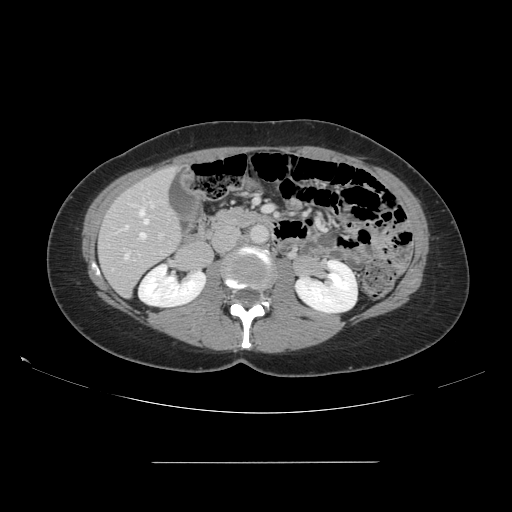
Contrast-enhanced abdominal CT, one axial slice. Position 60 of 151 along the scan axis. 120 kVp. Soft-tissue window (W 400 / L 40 HU). 512 × 512 image matrix, field of view 421 × 421 mm. Female patient, age 46 years. Case-level facts recorded for this patient, not image findings: diagnosis: colorectal cancer liver metastases, imaged before liver resection; multiple liver metastases: yes.
Structures marked on this image (manually delineated by an expert):
- hepatic veins: bounding box [x1, y1, x2, y2] px = [125, 207, 149, 260]
- liver: [99, 168, 181, 296]
- planned liver remnant (the part of the liver to remain after resection): [99, 168, 181, 296]
- portal vein (with intrahepatic branches): [159, 234, 162, 238]